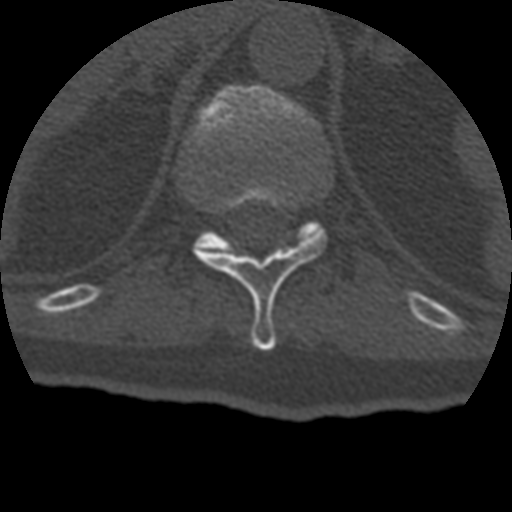
CT including the spine, one axial slice; position 187 of 399 along the scan axis; reconstruction kernel STANDARD; 120 kVp; bone window (W 1800 / L 400 HU); 512 × 512 image matrix, field of view 160 × 160 mm. Patient age 69 years. From the clinical record (not read from this slice): primary cancer: prostate.
Structures marked on this image (semi-automatic segmentation, software-assisted and operator-edited):
- T11 vertebra: box from (x=202, y=192) to (x=327, y=351) px
- T12 vertebra: (x=189, y=84)–(x=319, y=250)